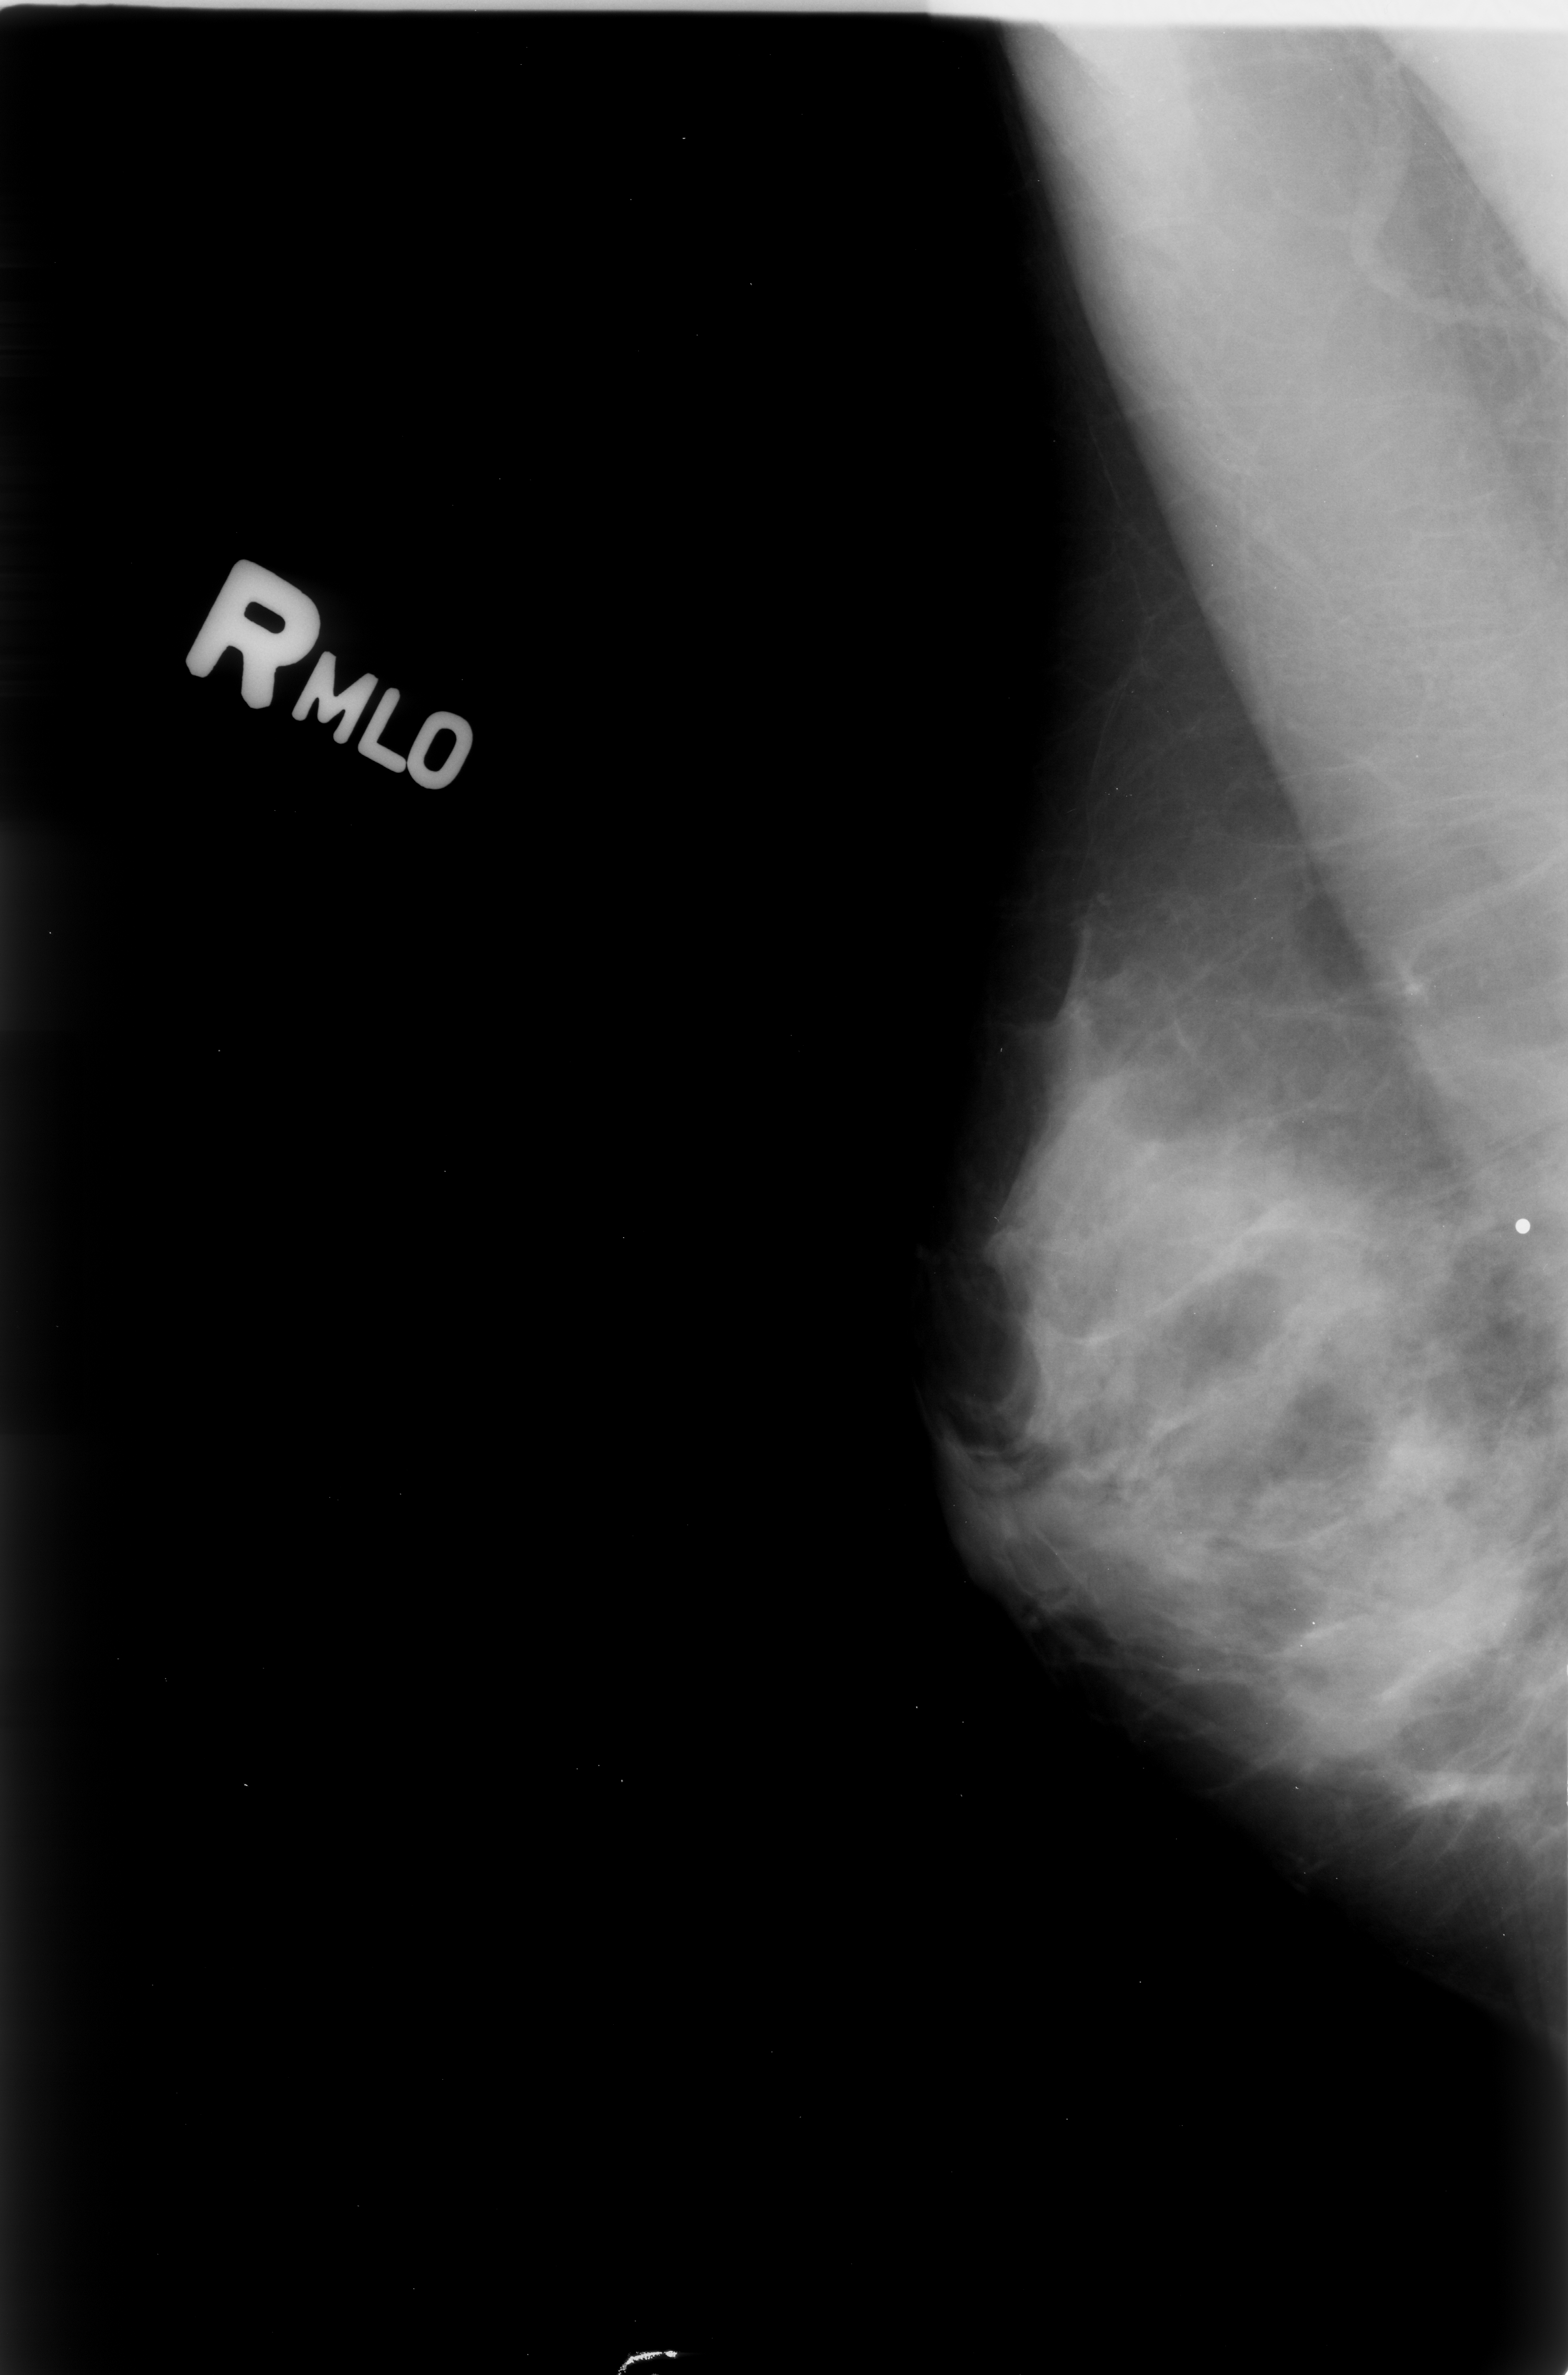
Scanned film-screen mammogram; right breast; mediolateral oblique (MLO) view; BI-RADS breast density category 4 (scale 1–4).
Marked findings (only marked abnormalities are described; nothing is implied about the rest of the image): calcifications, morphology pleomorphic, distribution clustered; BI-RADS assessment category 4; pathology result (as recorded, not read from the image): benign.